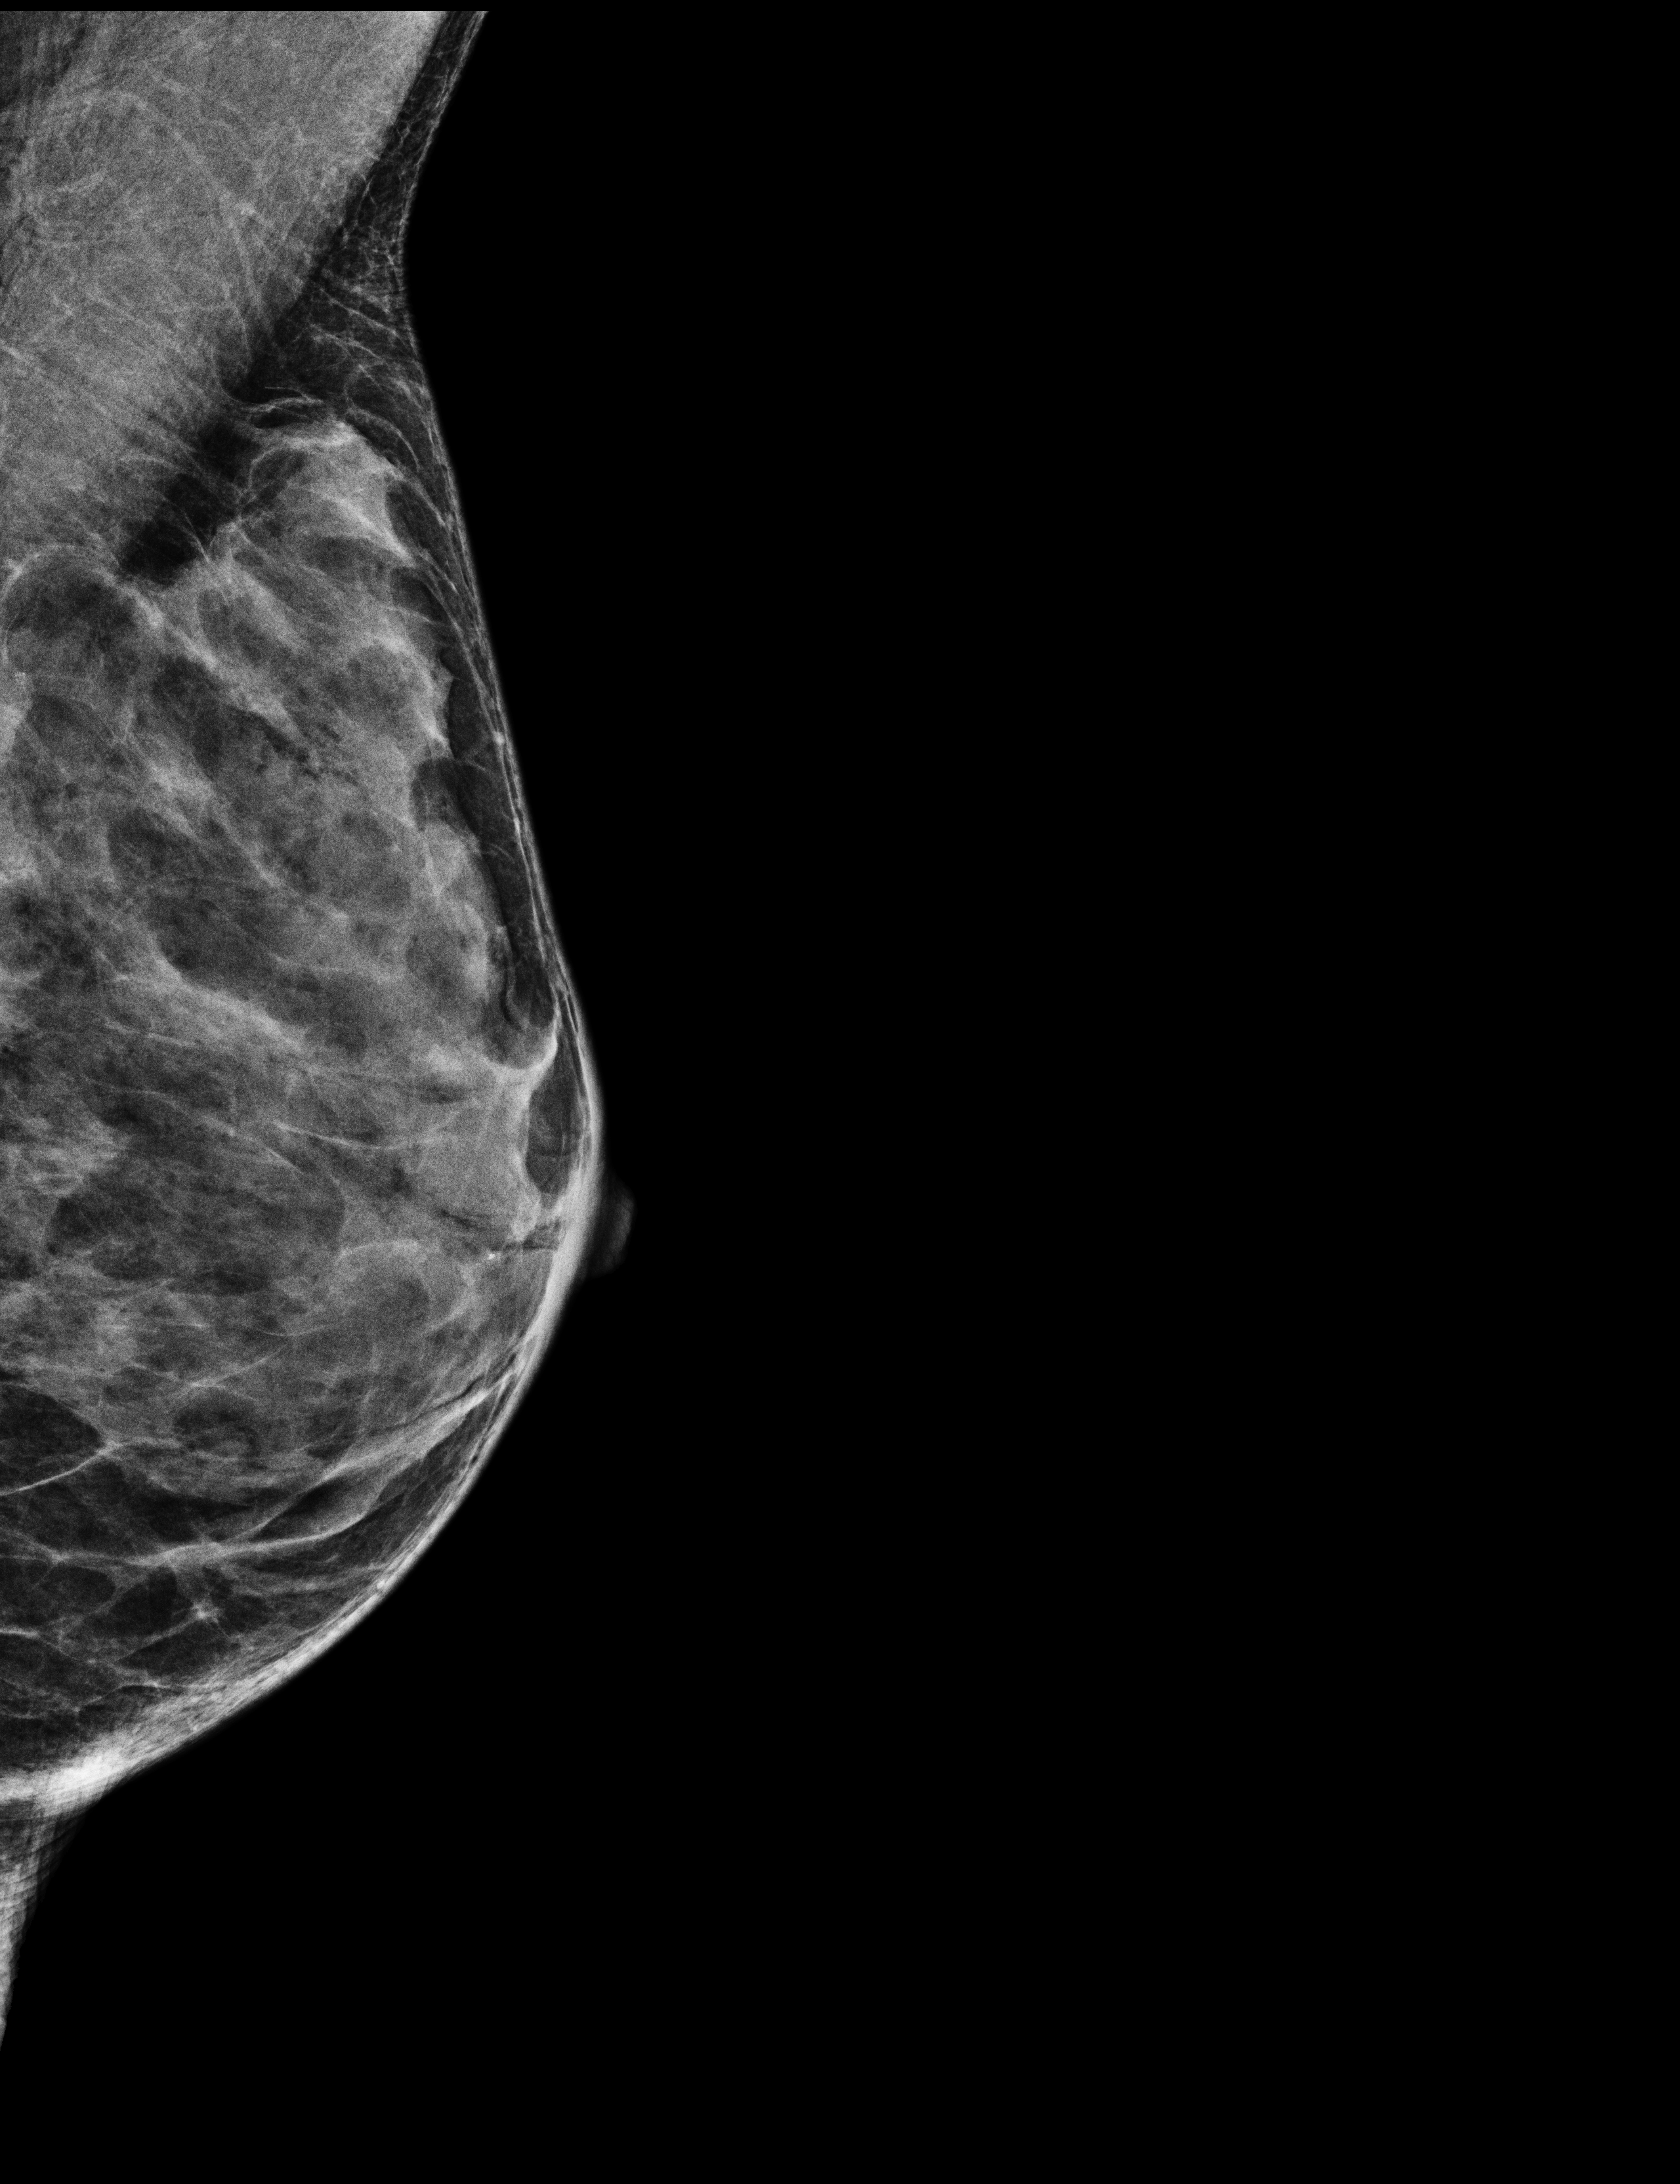
Digital mammogram (FFDM); left breast; MLO view; screening examination; system: Selenia Dimensions. Patient: female, 68 years.
- BI-RADS breast density category at the screening exam (both breasts, scale 1–4): 4
- final BI-RADS category for the screening round (tomosynthesis exam, both breasts): category 1
- recall: no recall after this screen